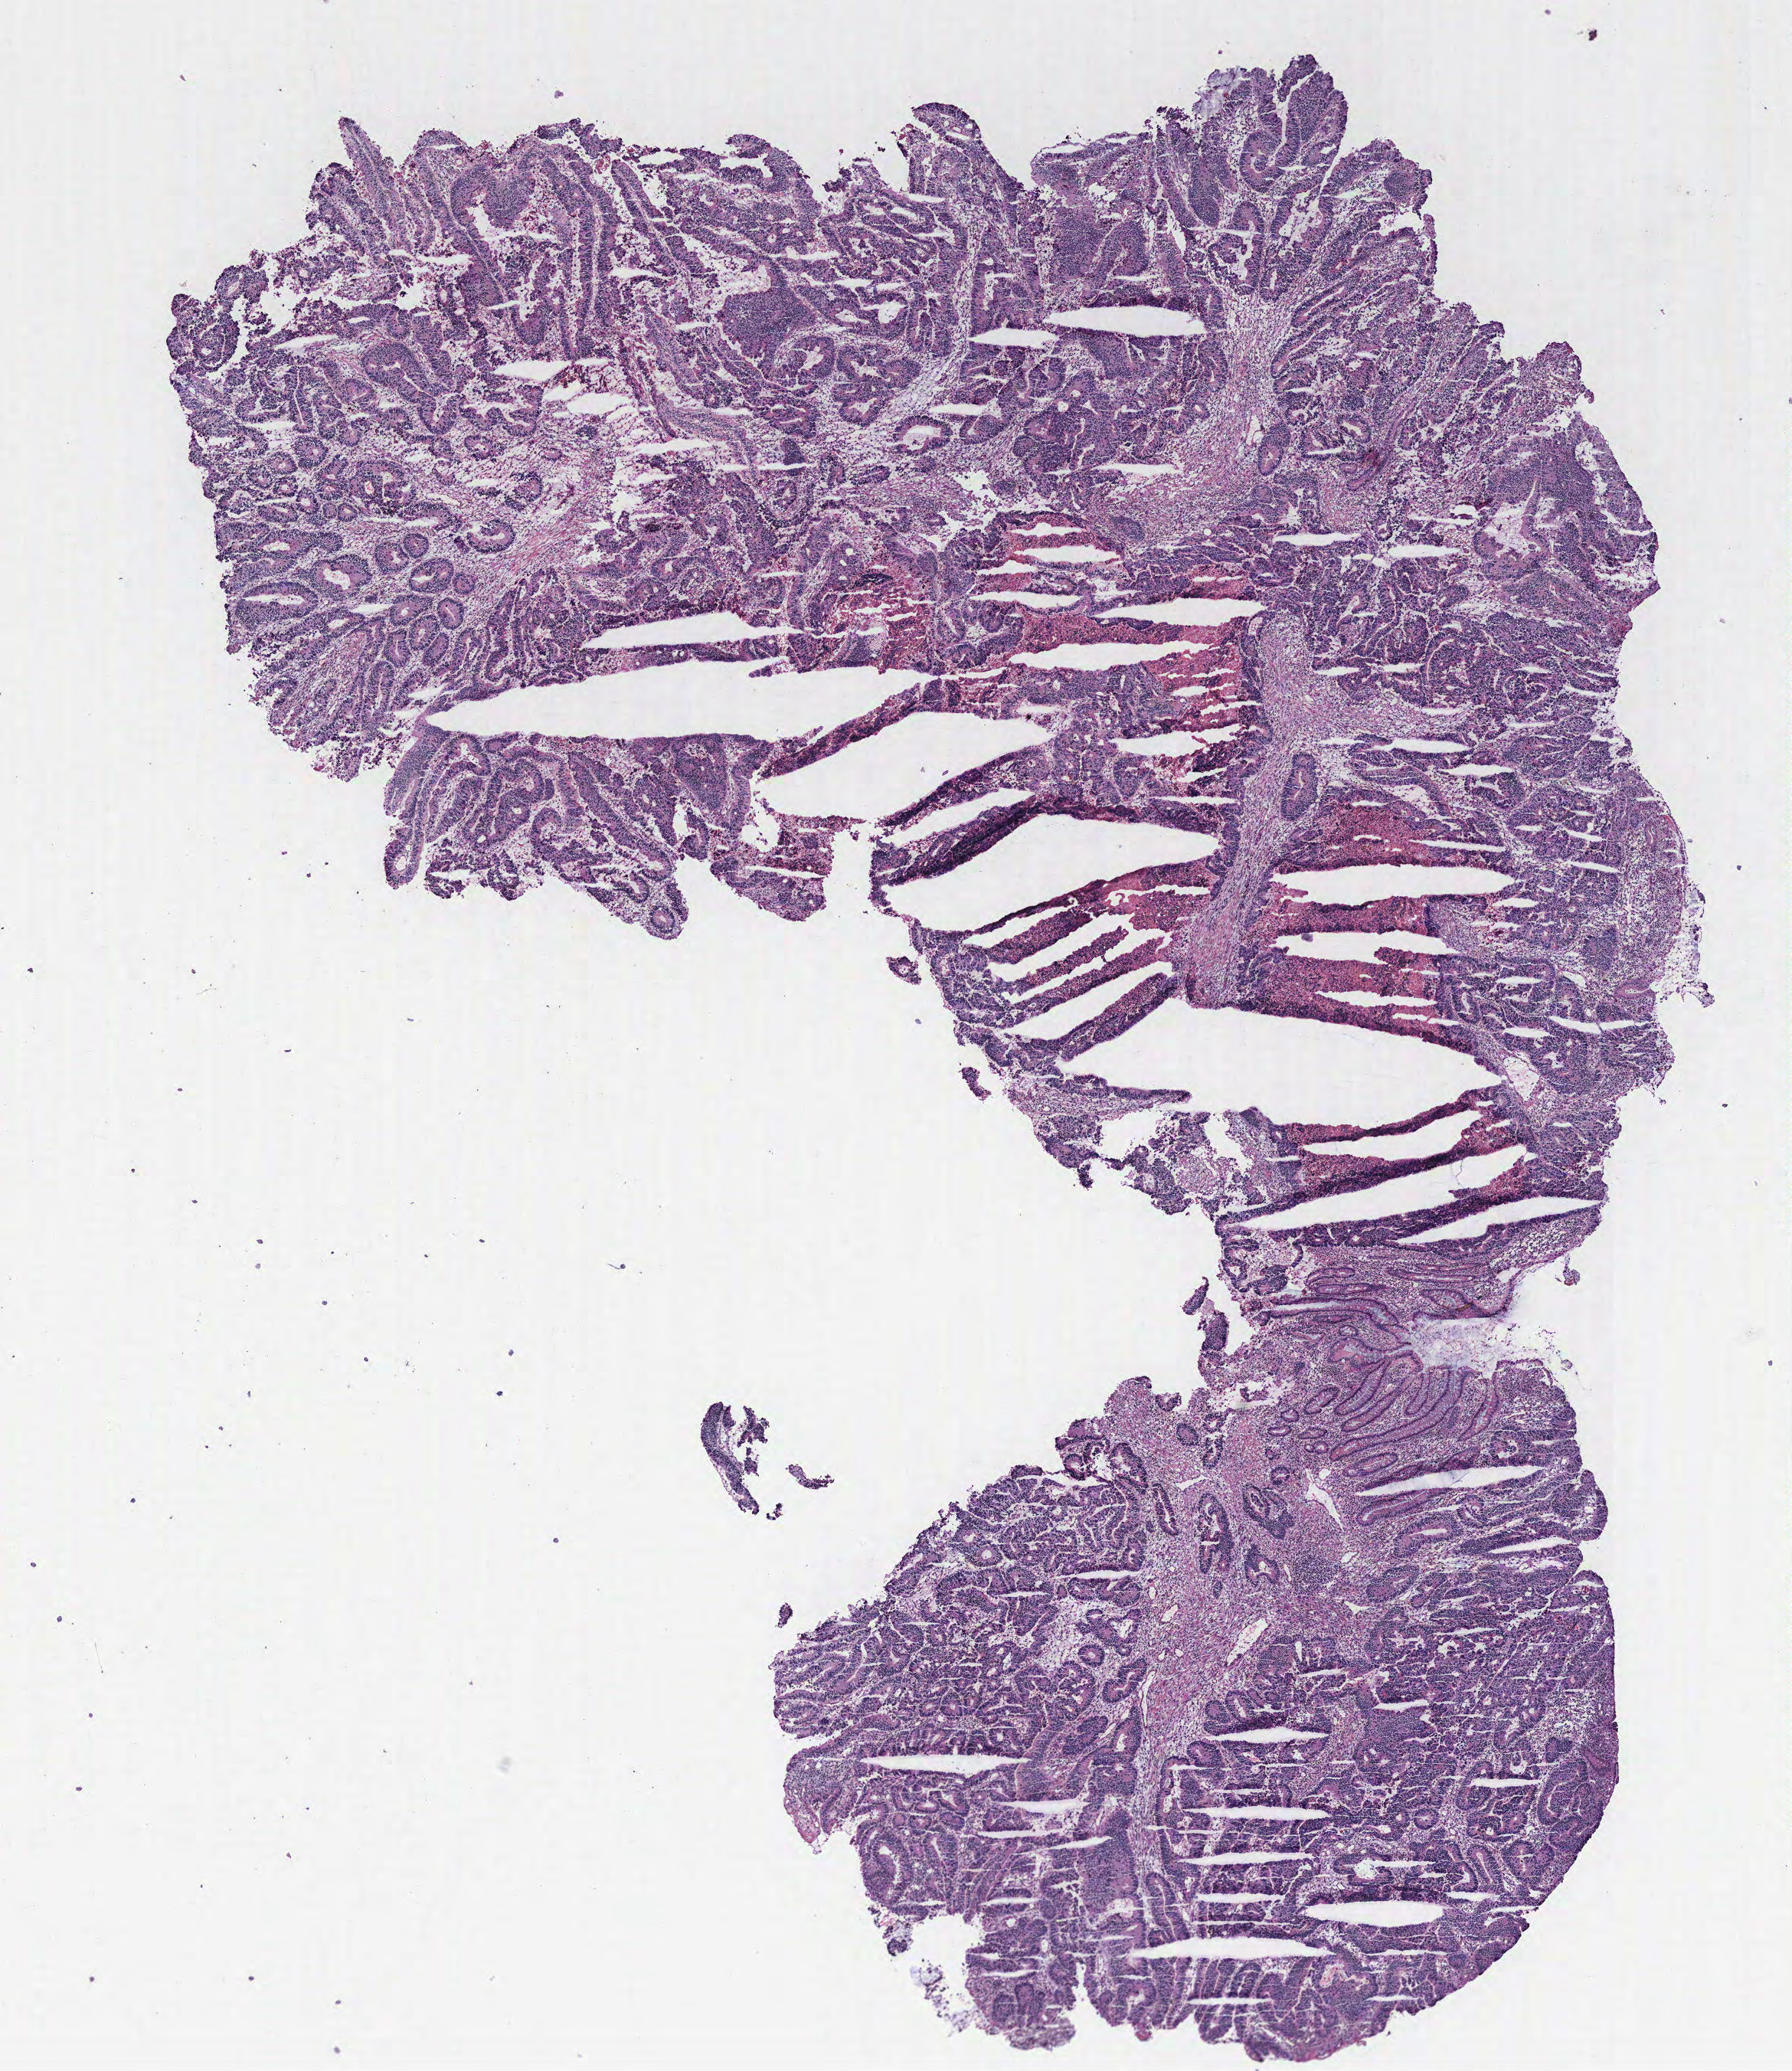
H&E-stained whole-slide image — shown as a low-resolution overview of the whole scanned area (about 9.4 x 10.8 mm, acquisition: 40x scan); colon, tissue type not recorded.
* patient diagnosis (cohort enrolment): colon cancer (colon)